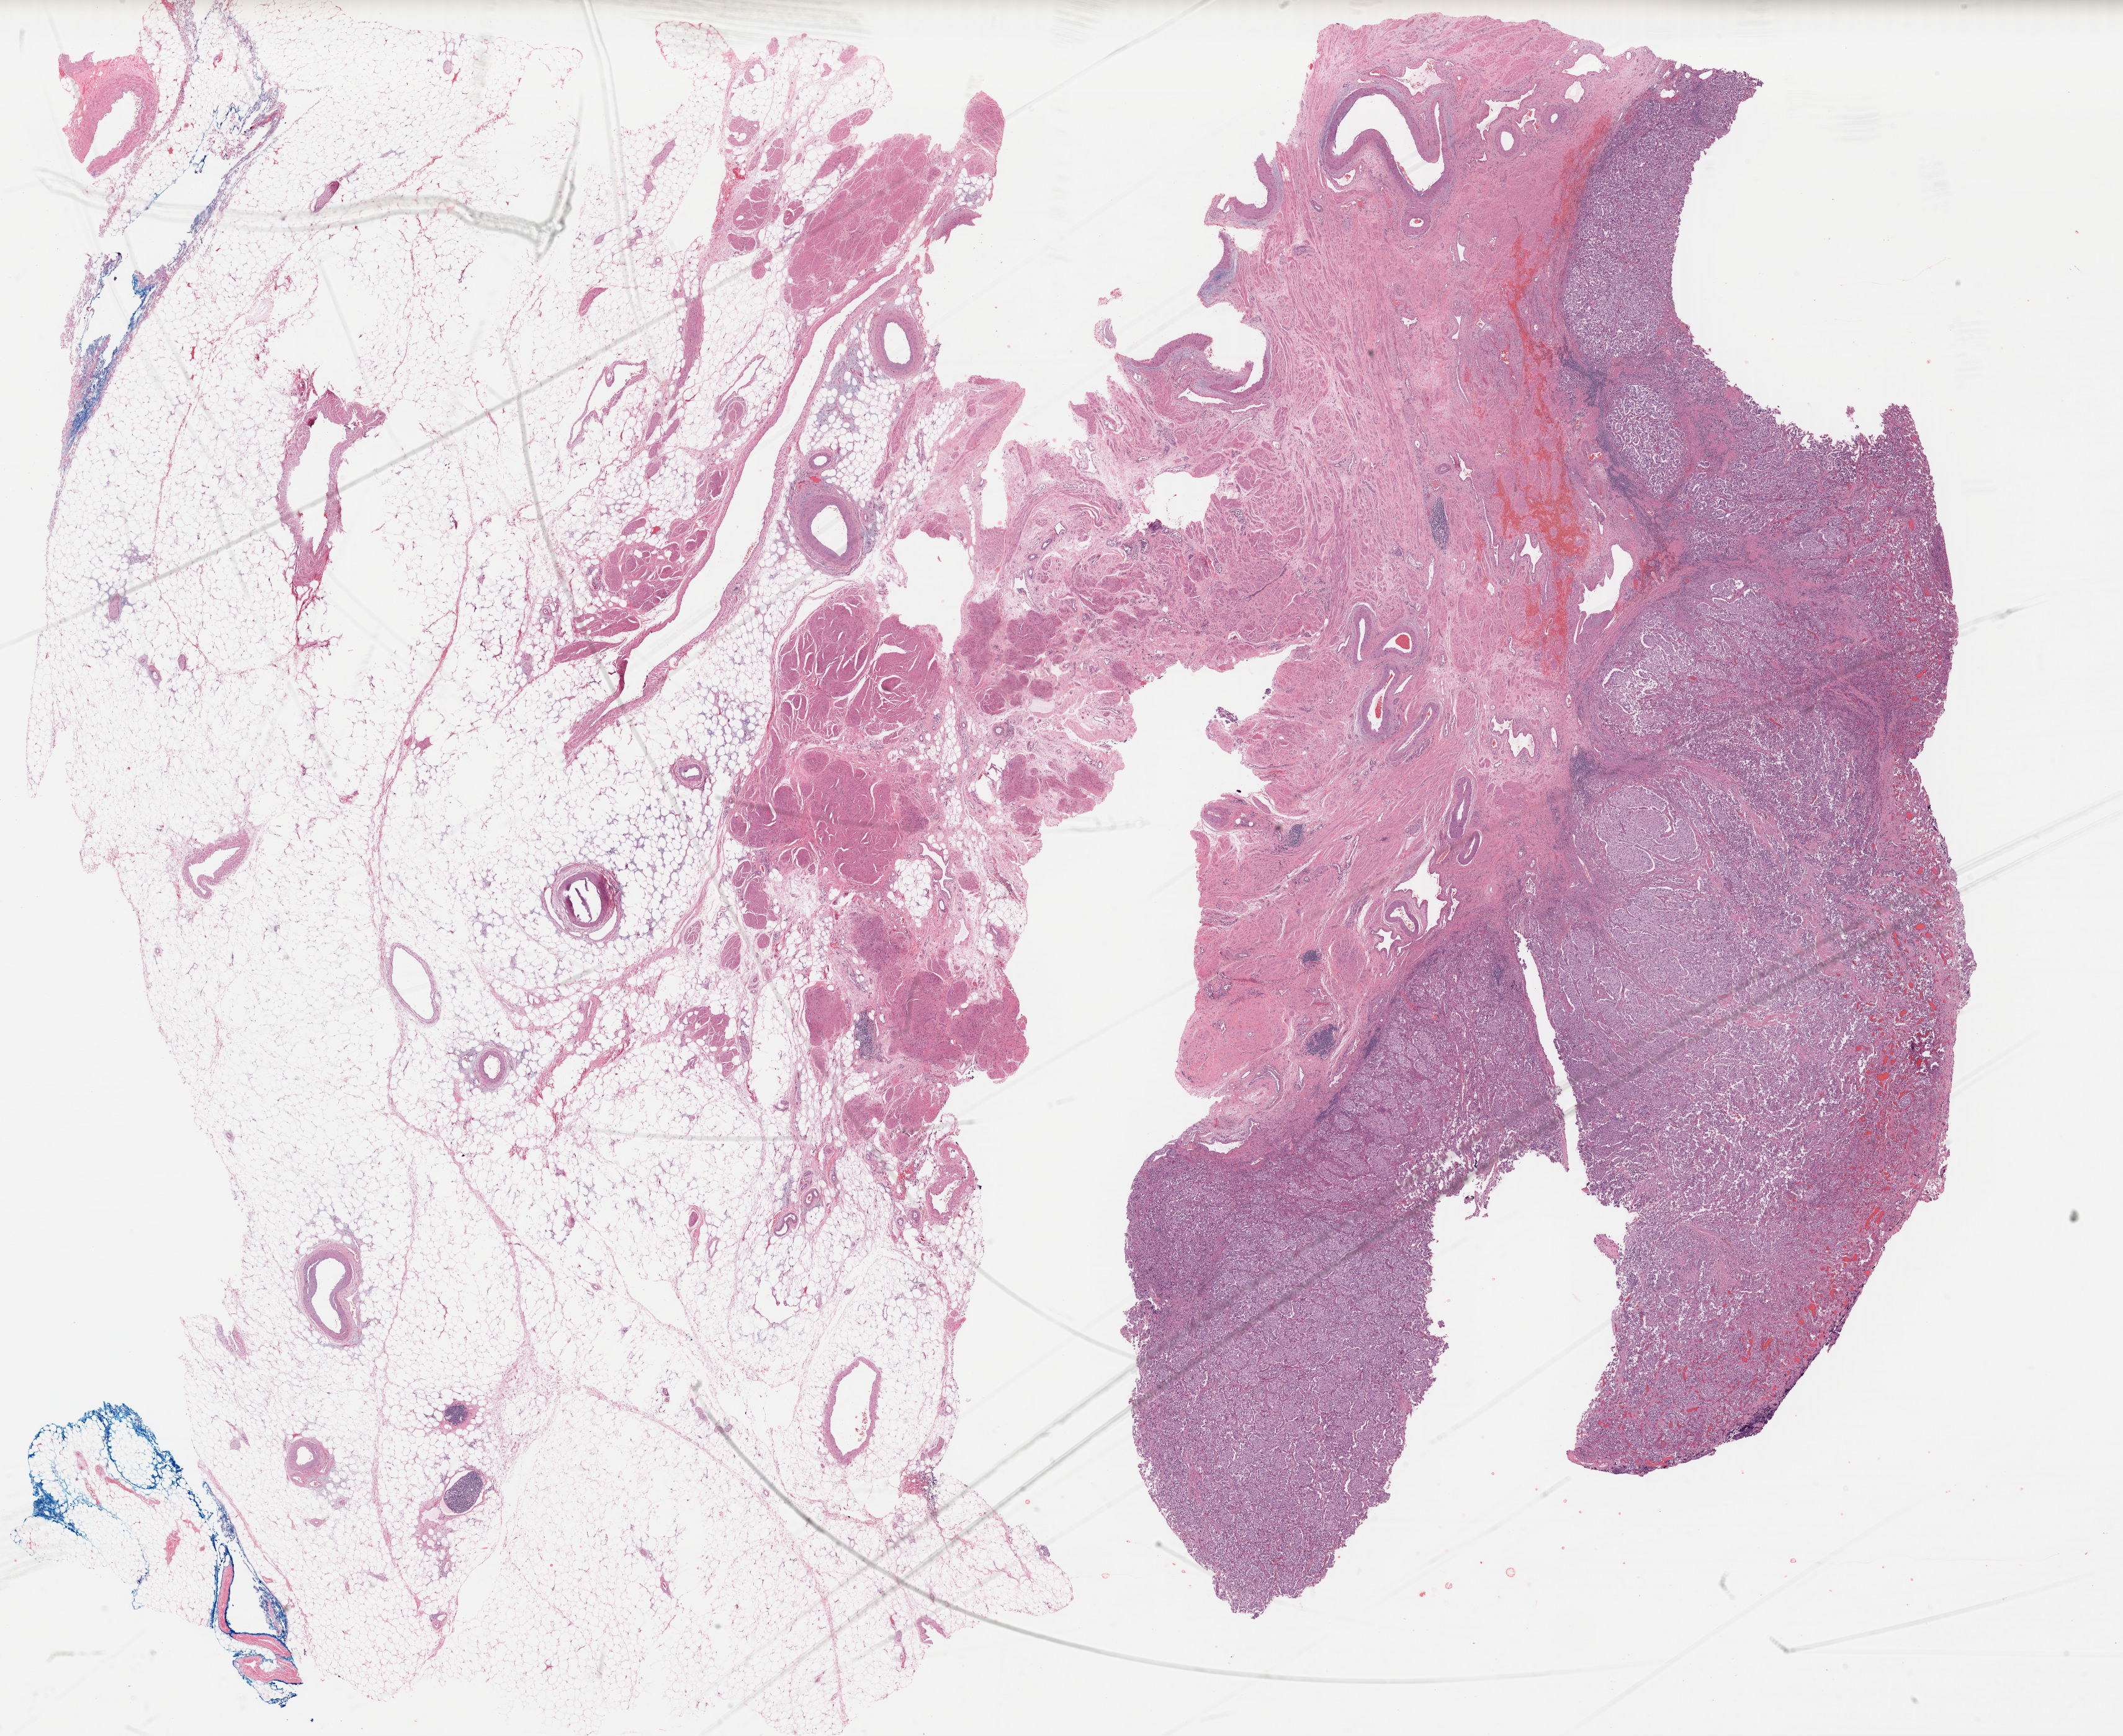
Digitized H&E-stained tissue section (whole slide) — whole scanned area (about 26.9 x 22.0 mm, from a 40x scan) shown as a low-resolution overview, formalin-fixed paraffin-embedded (FFPE) diagnostic section, bladder, primary tumour sample. Male, age 76 years at initial diagnosis. Histologic grade: high grade.
AJCC pathologic stage: IV (7th edition). Pathologic diagnosis: Transitional cell carcinoma. Lymph nodes positive (case pathology): 2 of 47 examined.